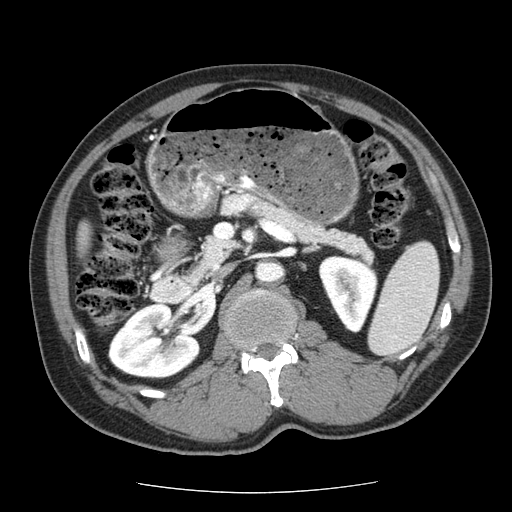
Contrast-enhanced abdominal CT (liver protocol), one axial slice. Slice 11 of 85 in the series (ordered by position). Reconstruction kernel STANDARD. 120 kVp. Soft-tissue window (W 400 / L 40 HU). 2.5 mm slice thickness. 512 × 512 image matrix. Case-level facts recorded for this patient, not image findings: diagnosis: hepatocellular carcinoma (patient treated with transarterial chemoembolisation; whether this scan precedes or follows treatment is not stated here); TNM stage (as recorded): Stage-IIIA; Child-Pugh class: A; tumour nodularity: multinodular; tumour size: 8 cm.
Structures marked on this image (semi-automatic segmentation, software-assisted and operator-edited):
- liver parenchyma outside the tumour (the mass and vessels are separate outlines, so this box may not span the whole liver): bounding box [x1, y1, x2, y2] px = [76, 222, 90, 254]